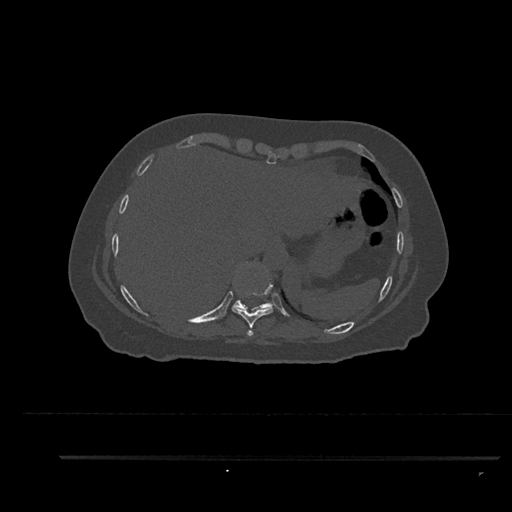
CT including the spine, one axial slice; slice 398 of 797 in the series (ordered by position); bone window (W 1800 / L 400 HU); 0.5 mm slice thickness; 512 × 512 image matrix. Female patient, age 44 years. From the clinical record (not read from this slice): primary cancer: renal.
Annotated regions visible in this slice (semi-automatic segmentation, software-assisted and operator-edited):
- T10 vertebra: bounding box (x1, y1, x2, y2) in pixels: (233, 261, 274, 310)
- T8 vertebra: (247, 330, 253, 336)
- T9 vertebra: (232, 269, 273, 329)